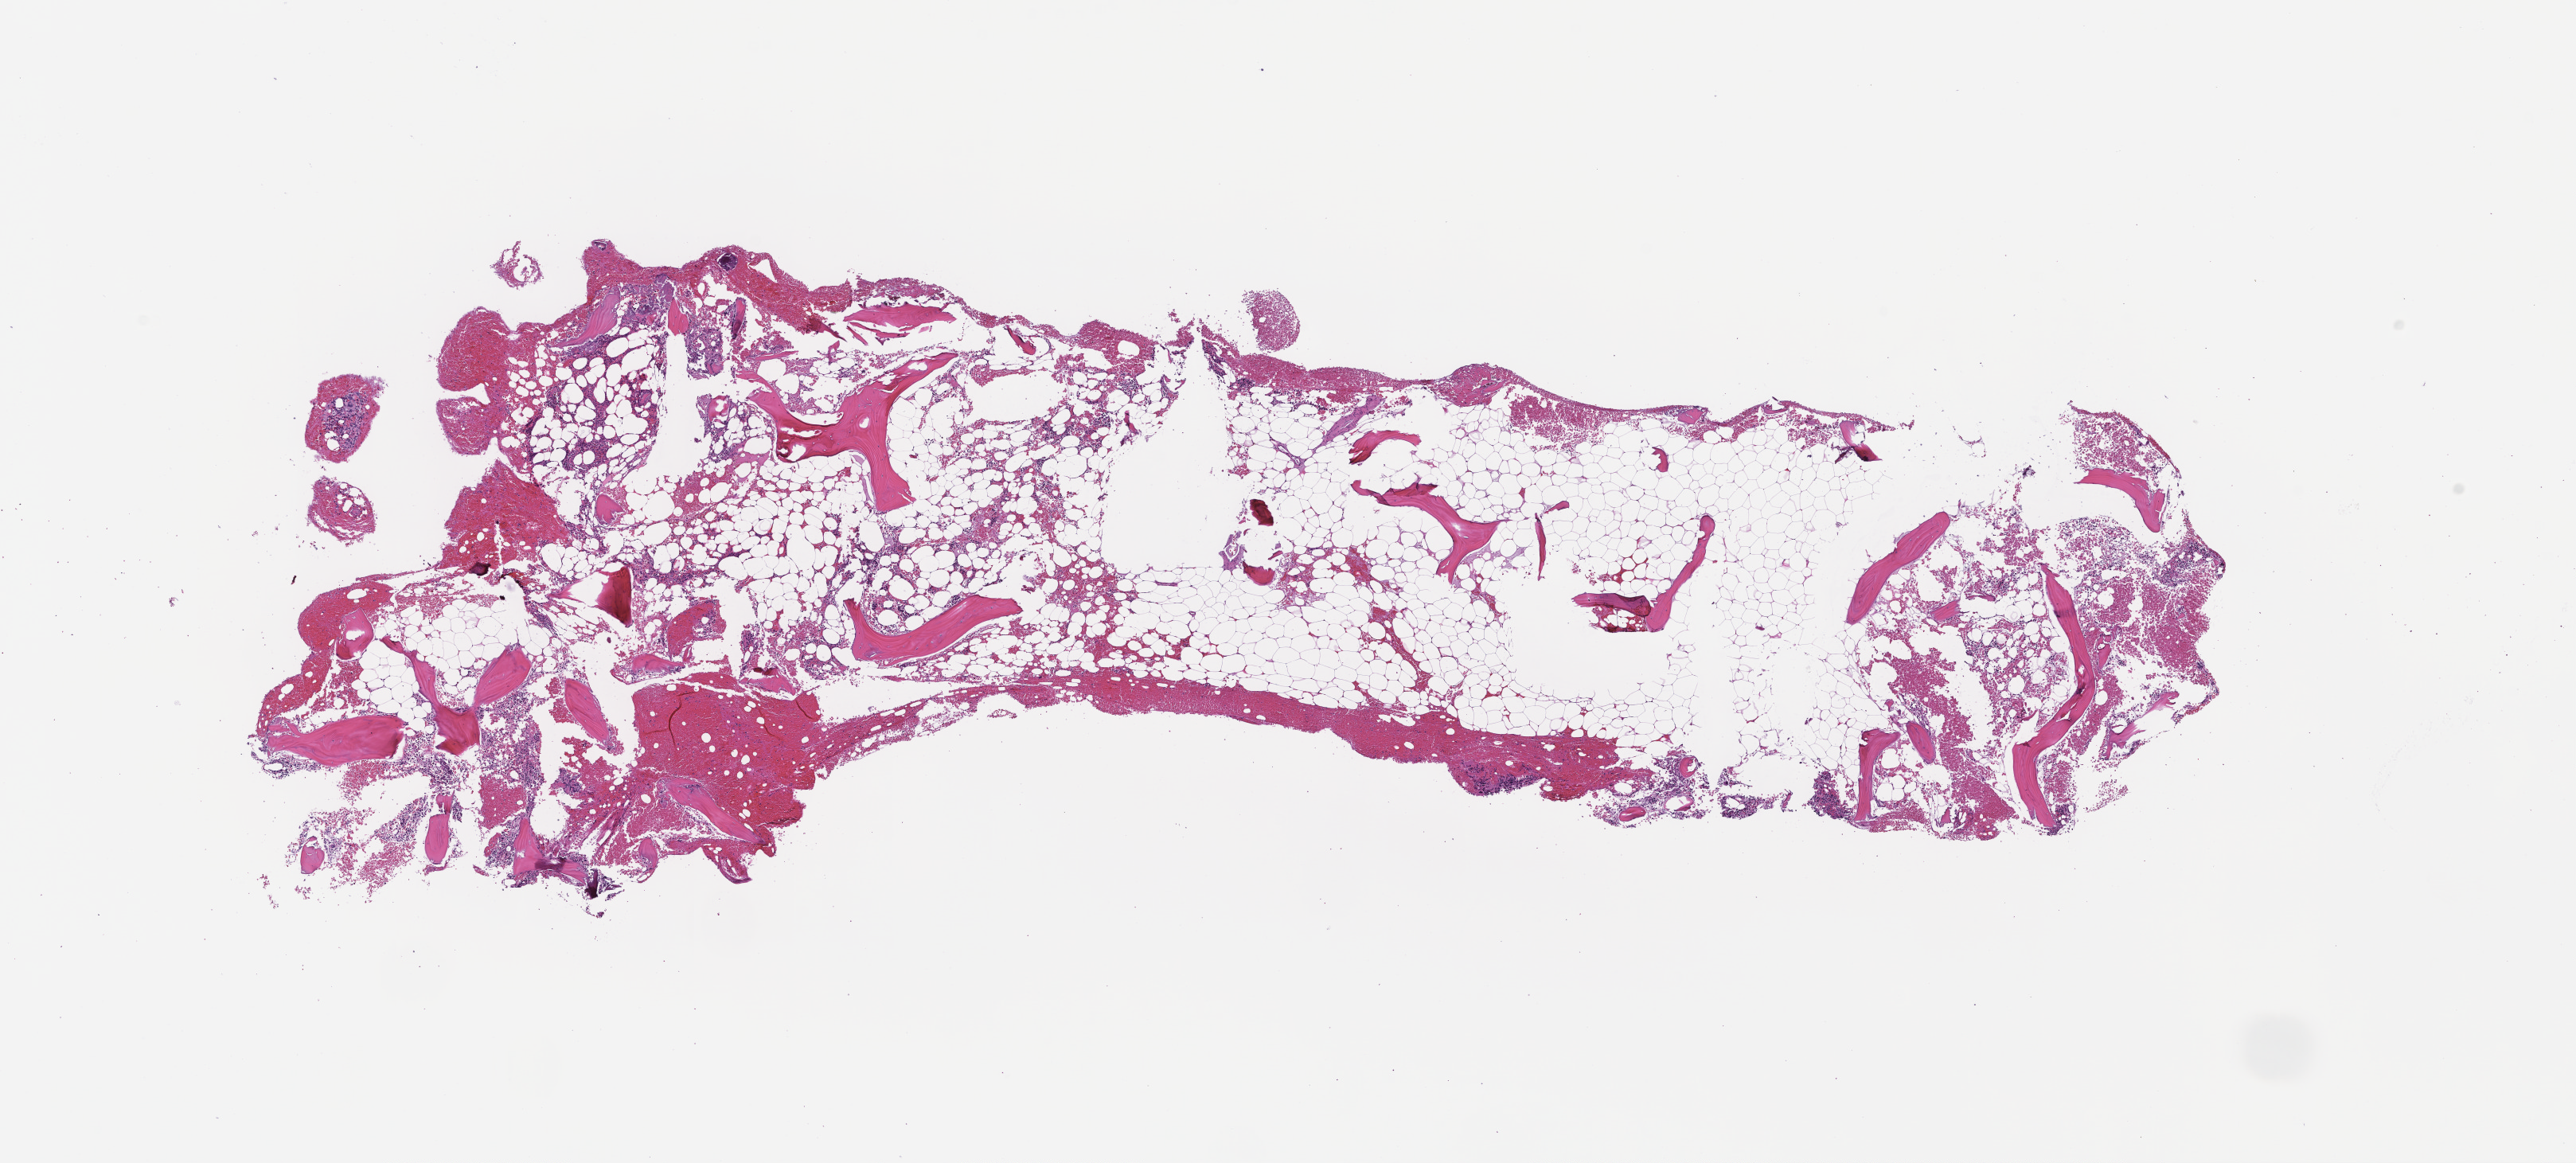
H&E whole-slide image, low-resolution overview of the scanned area, about 13.1 x 5.9 mm, formalin-fixed, paraffin-embedded (FFPE) tissue, tissue site: bone marrow, specimen time point: collected post-treatment, no progression. Patient sex: male.
This section: primary tumor. Diagnosis: Plasma Cell Myeloma.